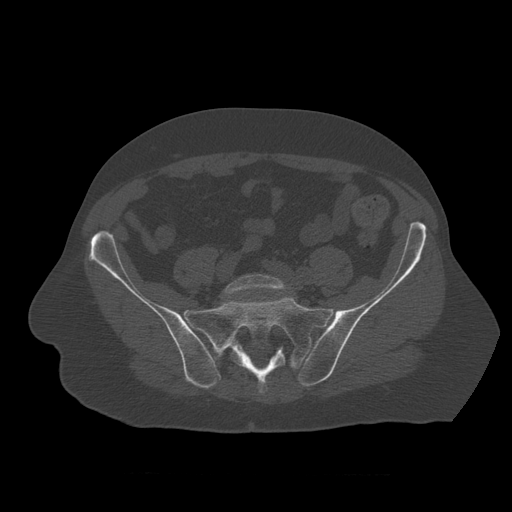
CT including the spine, one axial slice. Position 236 of 450 along the scan axis. 120 kVp. Bone window (W 1800 / L 400 HU). 1.25 mm slice thickness. 512 × 512 image matrix. Patient age 75 years. Case-level facts recorded for this patient, not image findings: primary cancer: prostate.
Structures marked on this image (semi-automatically segmented with operator editing):
- L5 vertebra: bounding box (x1, y1, x2, y2) in pixels: (223, 274, 285, 297)